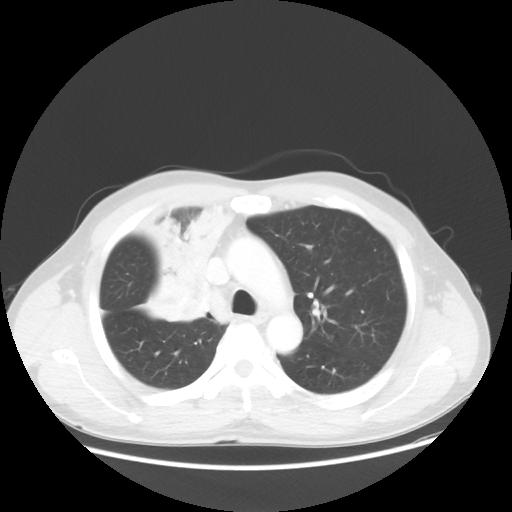
Chest CT, one axial slice; position 38 of 56 along the scan axis; reconstruction kernel STANDARD; 100 kVp; lung window (W 1500 / L -600 HU); 512 × 512 image matrix, field of view 398 × 398 mm. Patient: male, 60 years. Case-level facts recorded for this patient, not image findings: clinical TNM (as recorded): T2a N1 M0.
Annotated regions visible in this slice (bounding box drawn by a radiologist):
- lung tumour (recorded histology: squamous cell carcinoma): bounding box [x1, y1, x2, y2] px = [119, 176, 249, 335]